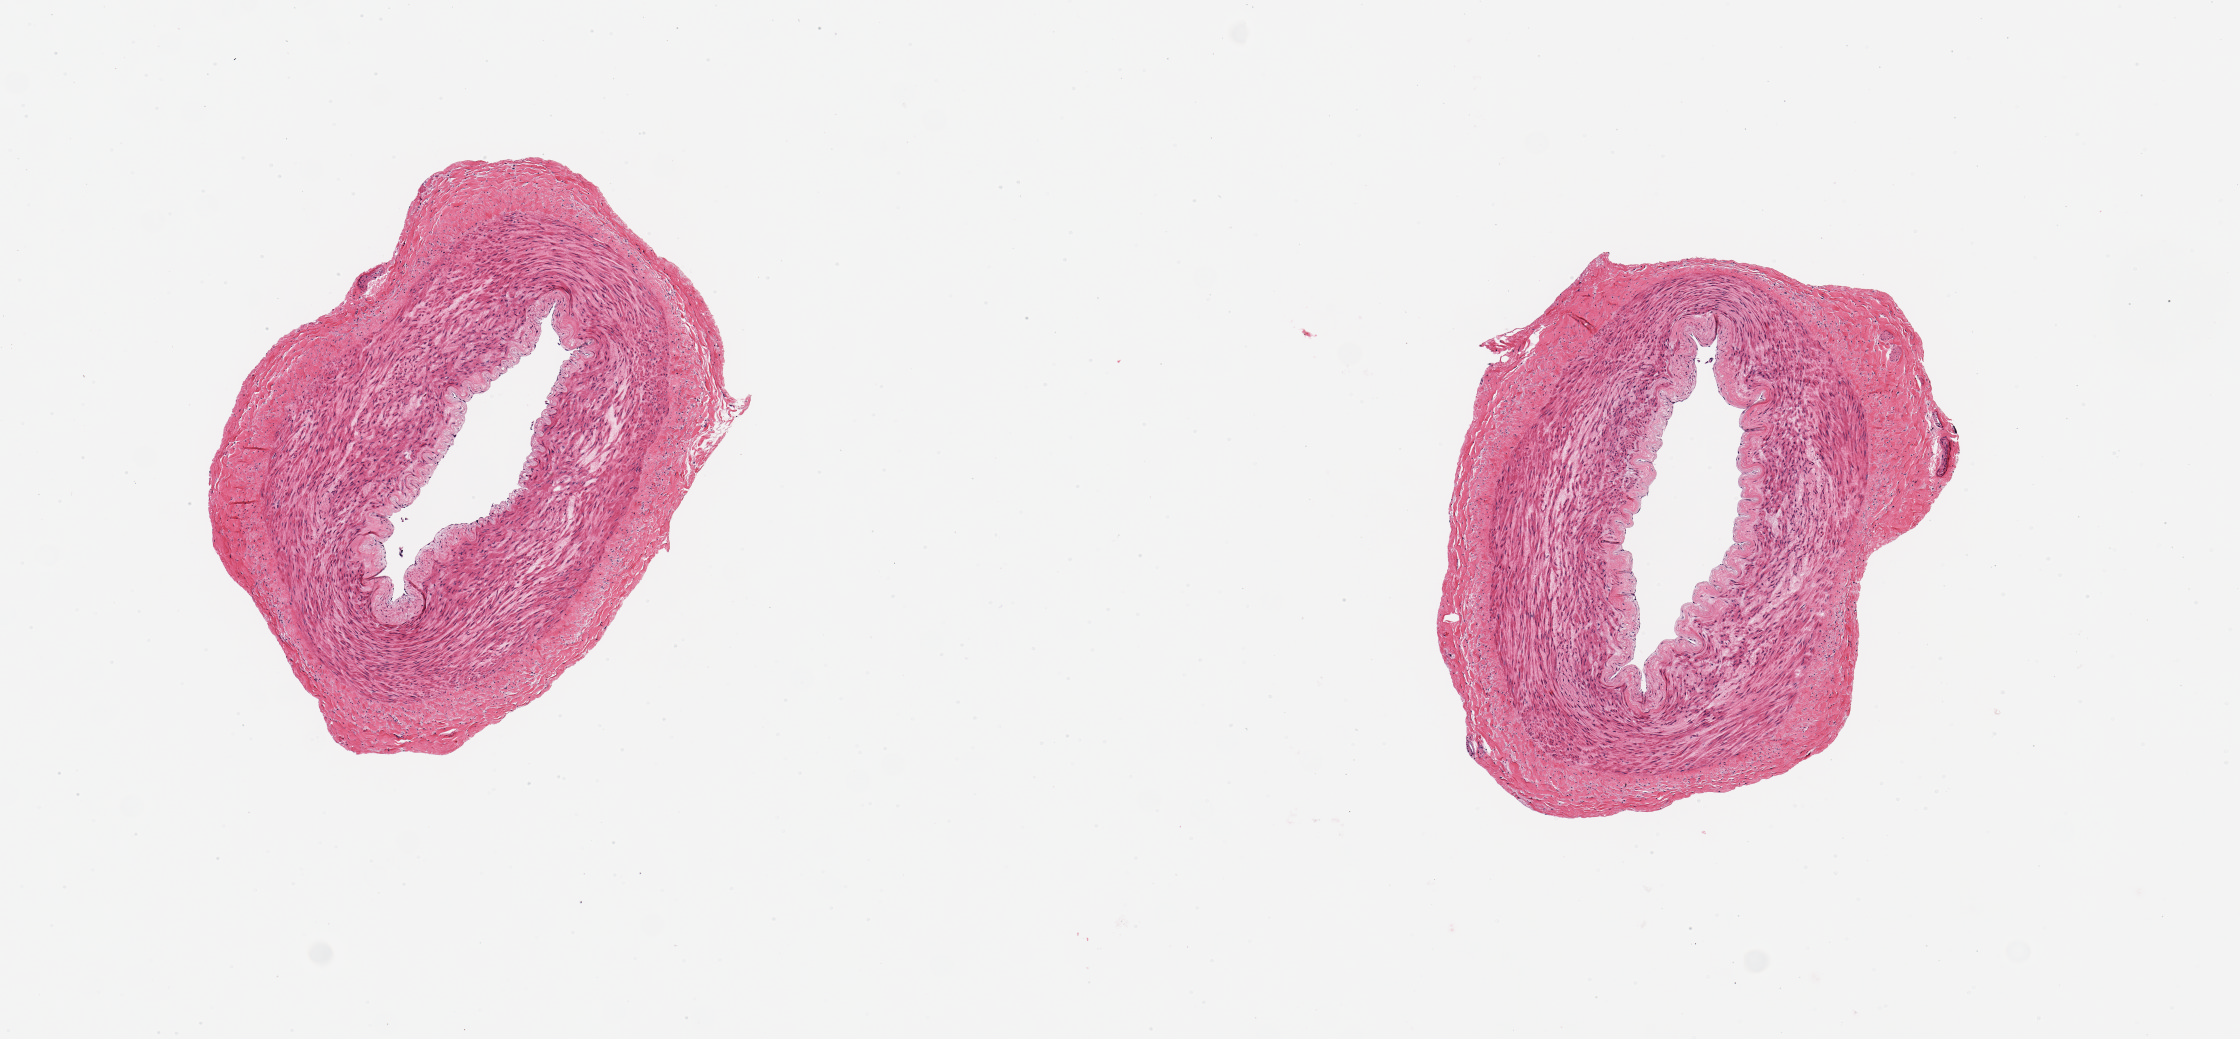
Digitized haematoxylin and eosin-stained section — shown as a low-resolution overview of the whole scanned area (about 8.9 x 4.1 mm), PAXgene-fixed, paraffin-embedded tissue, sampled site (target tissue): tibial artery, tissue donor sample. Donor: female.
Pathologist's review note for this sample: 2 ~2mm d aliquots, clean specimens.